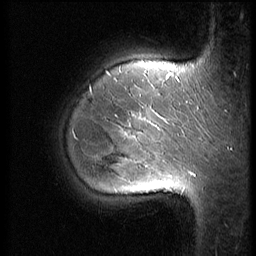
Breast MRI (dynamic contrast-enhanced), one sagittal slice. Slice 49 of 56 in the series (ordered by position). 3 images stored at this slice position (order not interpretable as contrast timing). 1.5 T. TE 4.2 ms, TR 9 ms. 2.5 mm slice thickness. 256 × 256 image matrix, field of view 180 × 180 mm. Female patient, age 35 years. Case-level facts recorded for this patient, not image findings: setting: breast cancer imaged before/during neoadjuvant chemotherapy; receptor status: HR-positive, HER2-negative.
Annotated regions visible in this slice (semi-automatically segmented with operator editing):
- analysis volume of interest (the breast-tissue region the enhancement analysis was run in; not a lesion): bounding box <63,60,190,218> (left, top, right, bottom; pixels)
- tumour enhancement mask (voxels above the 140 % enhancement threshold inside the analysis volume of interest): <132,115,159,129>